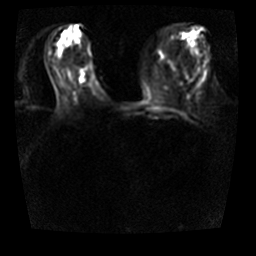
Breast MRI, one axial slice; slice 14 of 32 in the series (ordered by position); diffusion-weighted series; image 2 of 4 stored at this slice position (different b-values; order by instance number); 3 T; 5 mm slice thickness; 256 × 256 image matrix. Female patient.
Annotated regions visible in this slice (expert manual segmentation):
- tumour on diffusion-weighted imaging: bounding box (x1, y1, x2, y2) in pixels: (80, 68, 86, 73)